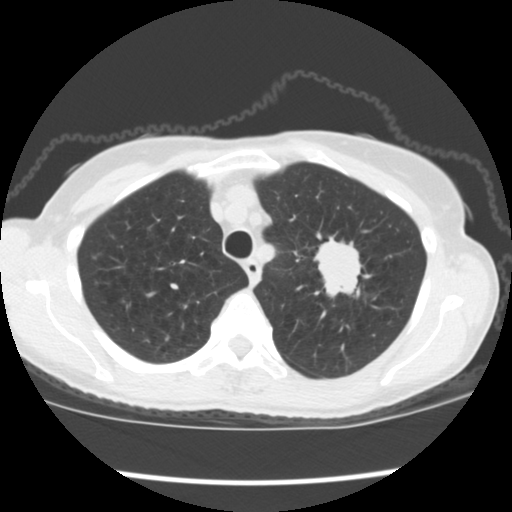
Low-dose screening chest CT, one axial slice. Slice 144 of 176 in the series (ordered by position). Reconstruction kernel STANDARD. 120 kVp. Lung window (W 1500 / L -600 HU). 2.5 mm slice thickness. 512 × 512 image matrix.
Annotated regions visible in this slice (outlined manually by an expert reader):
- lesion 1 (tumor, upper lobe of left lung): box from (x=314, y=238) to (x=361, y=298) px